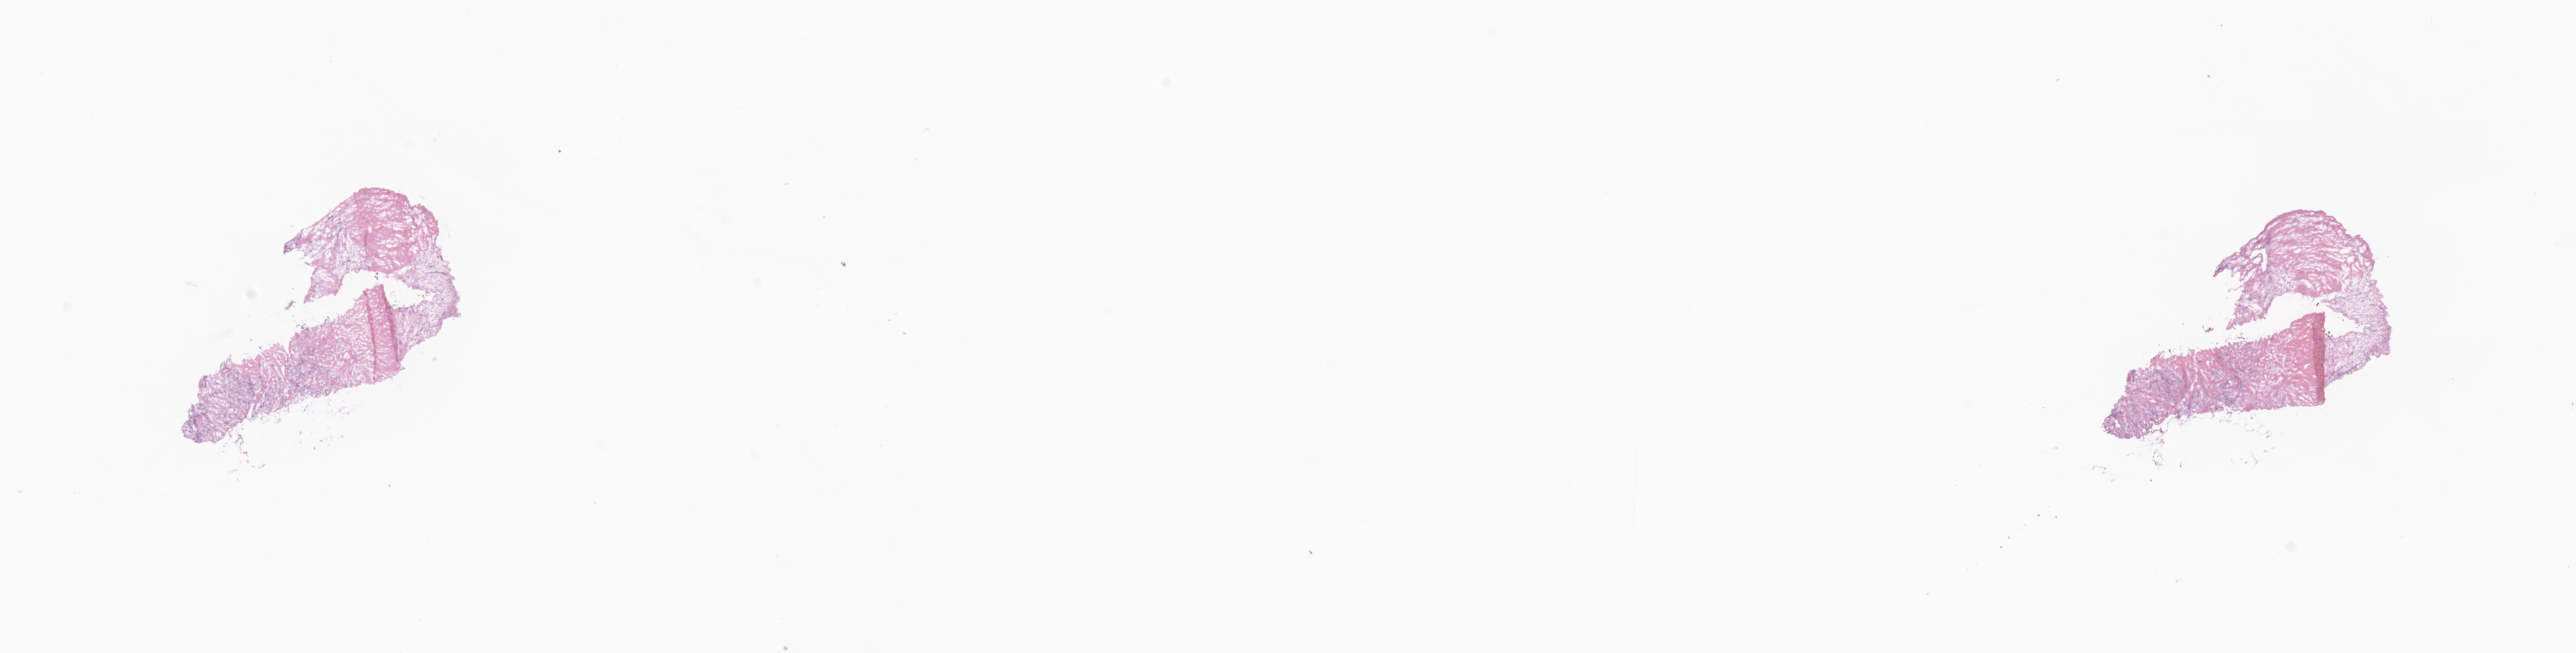
Digitized haematoxylin and eosin-stained section — low-resolution overview of the scanned area, about 25.7 x 6.5 mm, cryosection, primary tumor, site: breast (left). Female, age 50 years at initial diagnosis. Pathologist review of this section (percent, as recorded): tumor cells 40%, tumor nuclei 67%, stromal cells 57%, necrosis 3%, normal cells 0%. Inflammatory infiltration, as recorded: lymphocyte infiltration 0%, monocyte infiltration 0%, neutrophil infiltration 0%.
• diagnosis: Lobular carcinoma, NOS